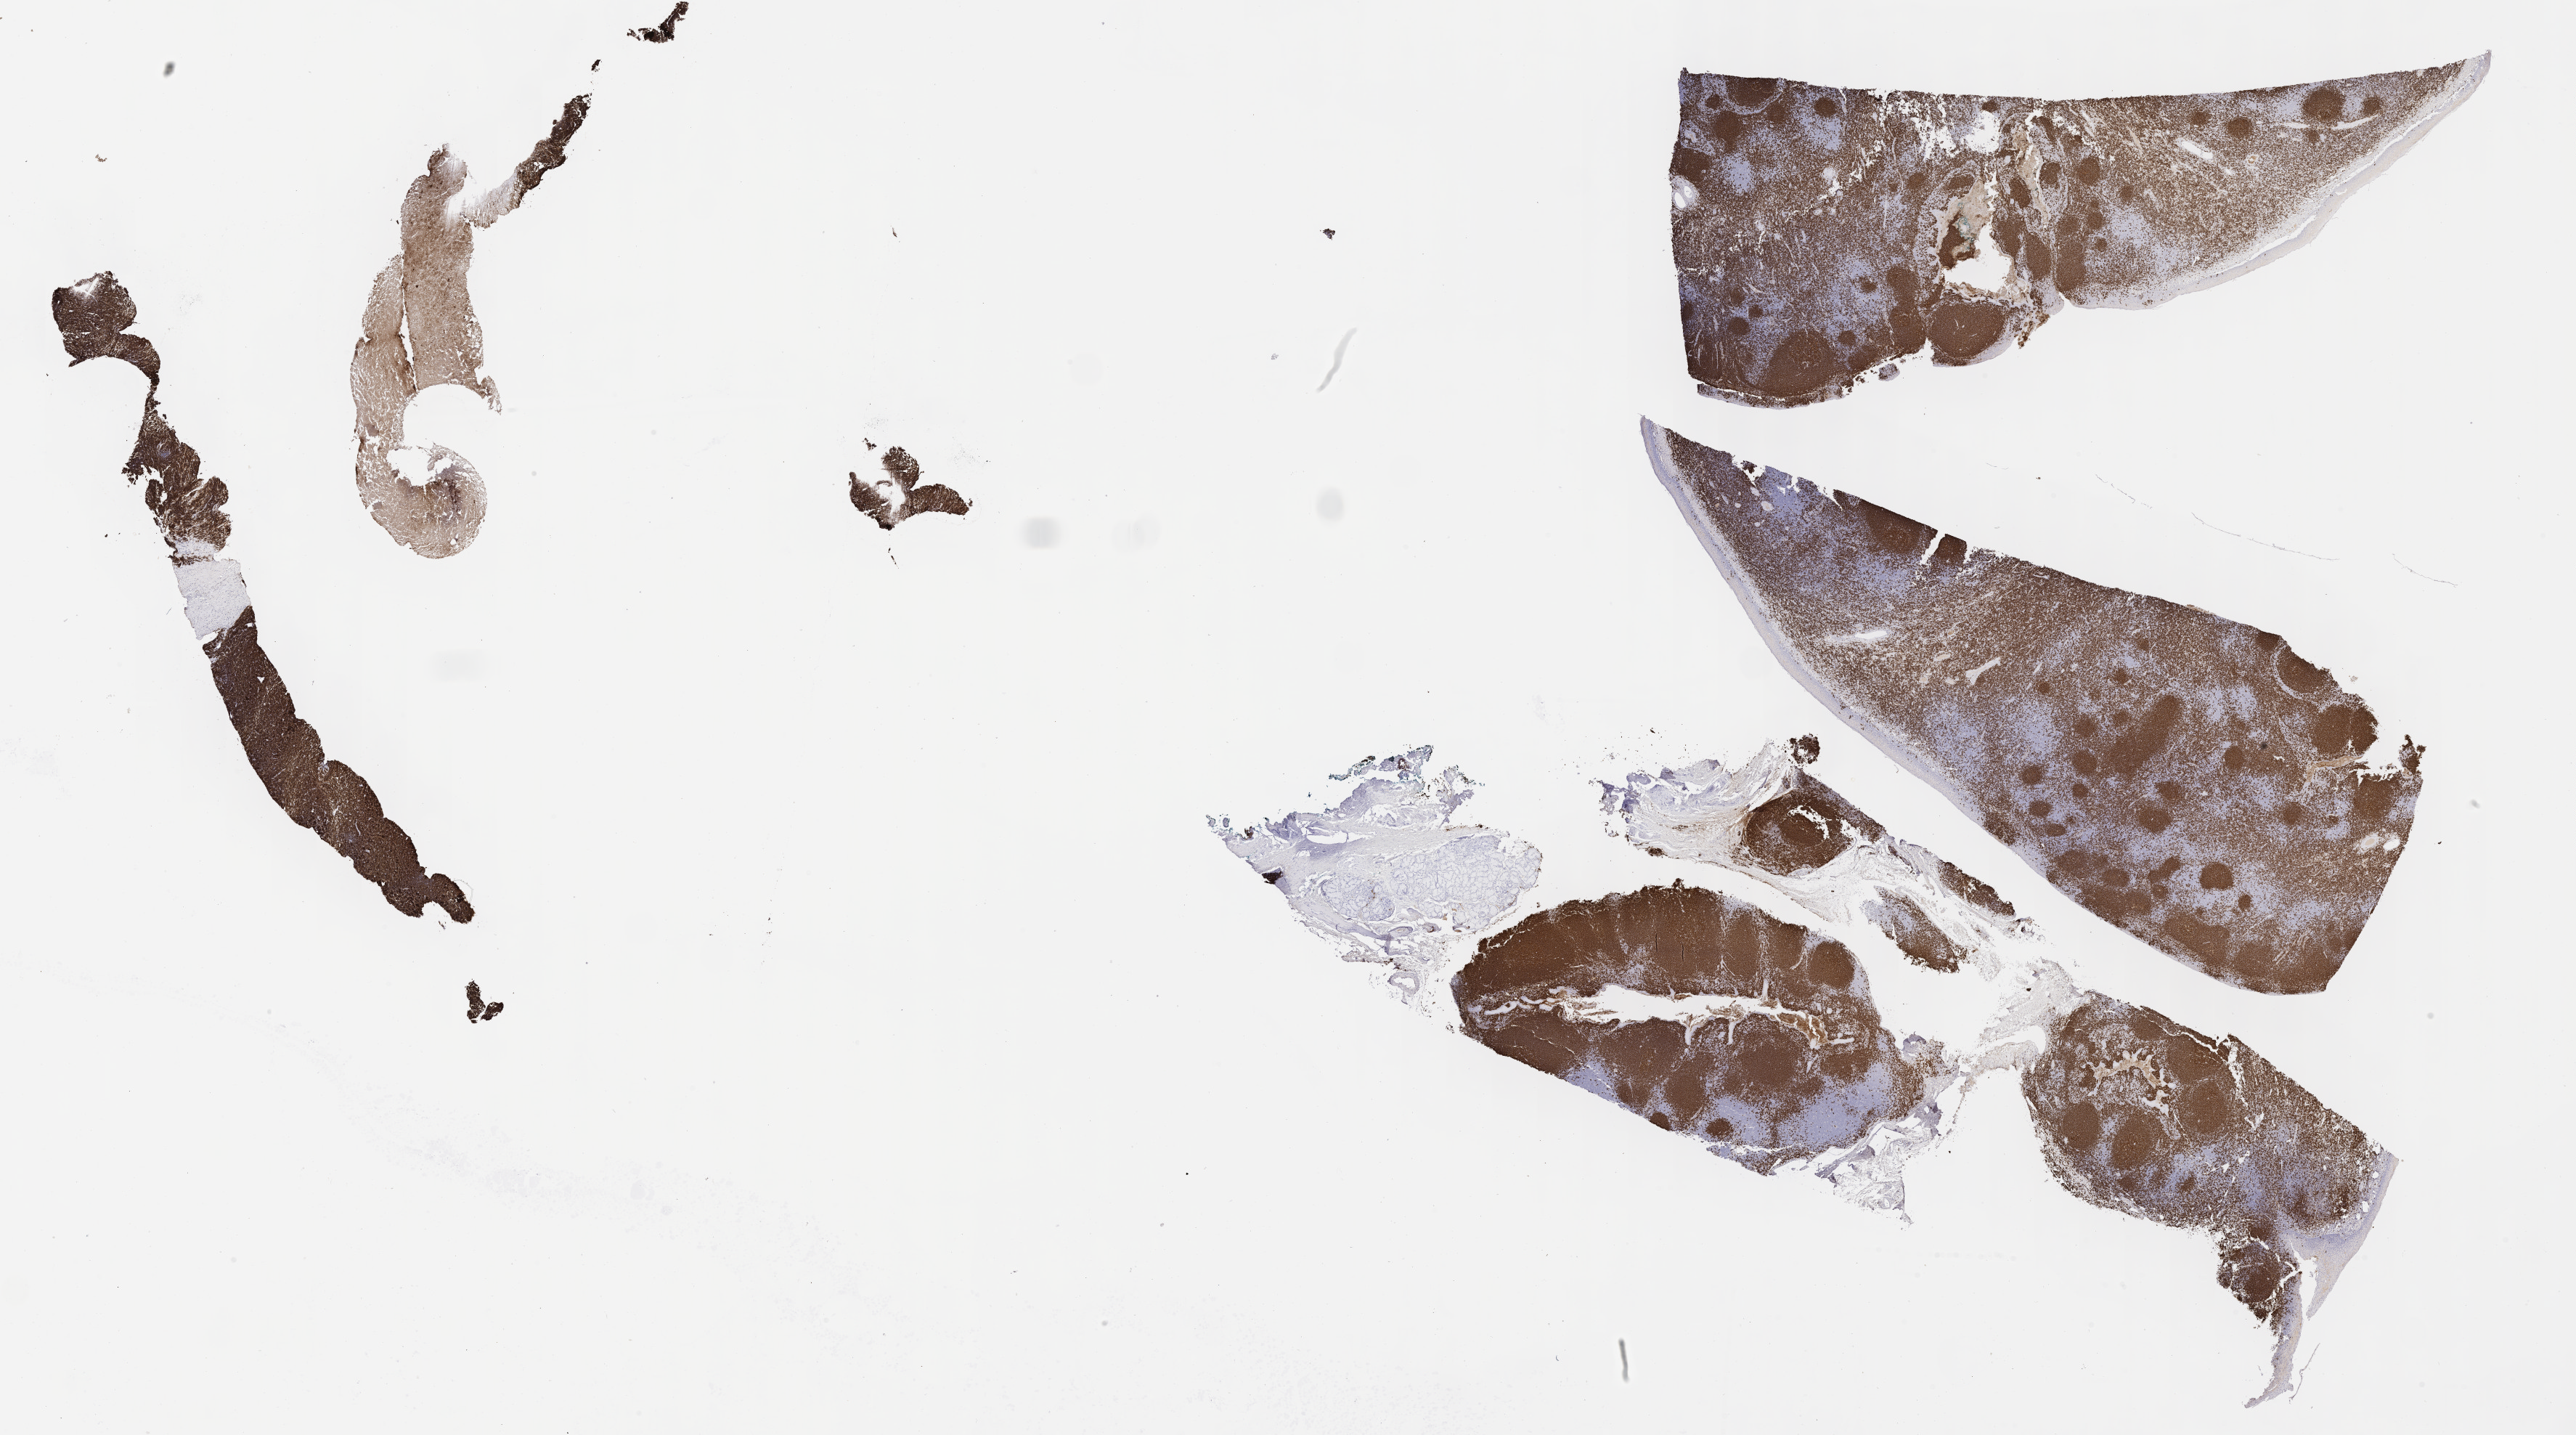
IHC for CD20, whole-slide image — whole scanned area (about 28.7 x 16.0 mm) shown as a low-resolution overview, tumor tissue. Patient male; age 10 years.
- histologic diagnosis: Burkitt lymphoma, NOS